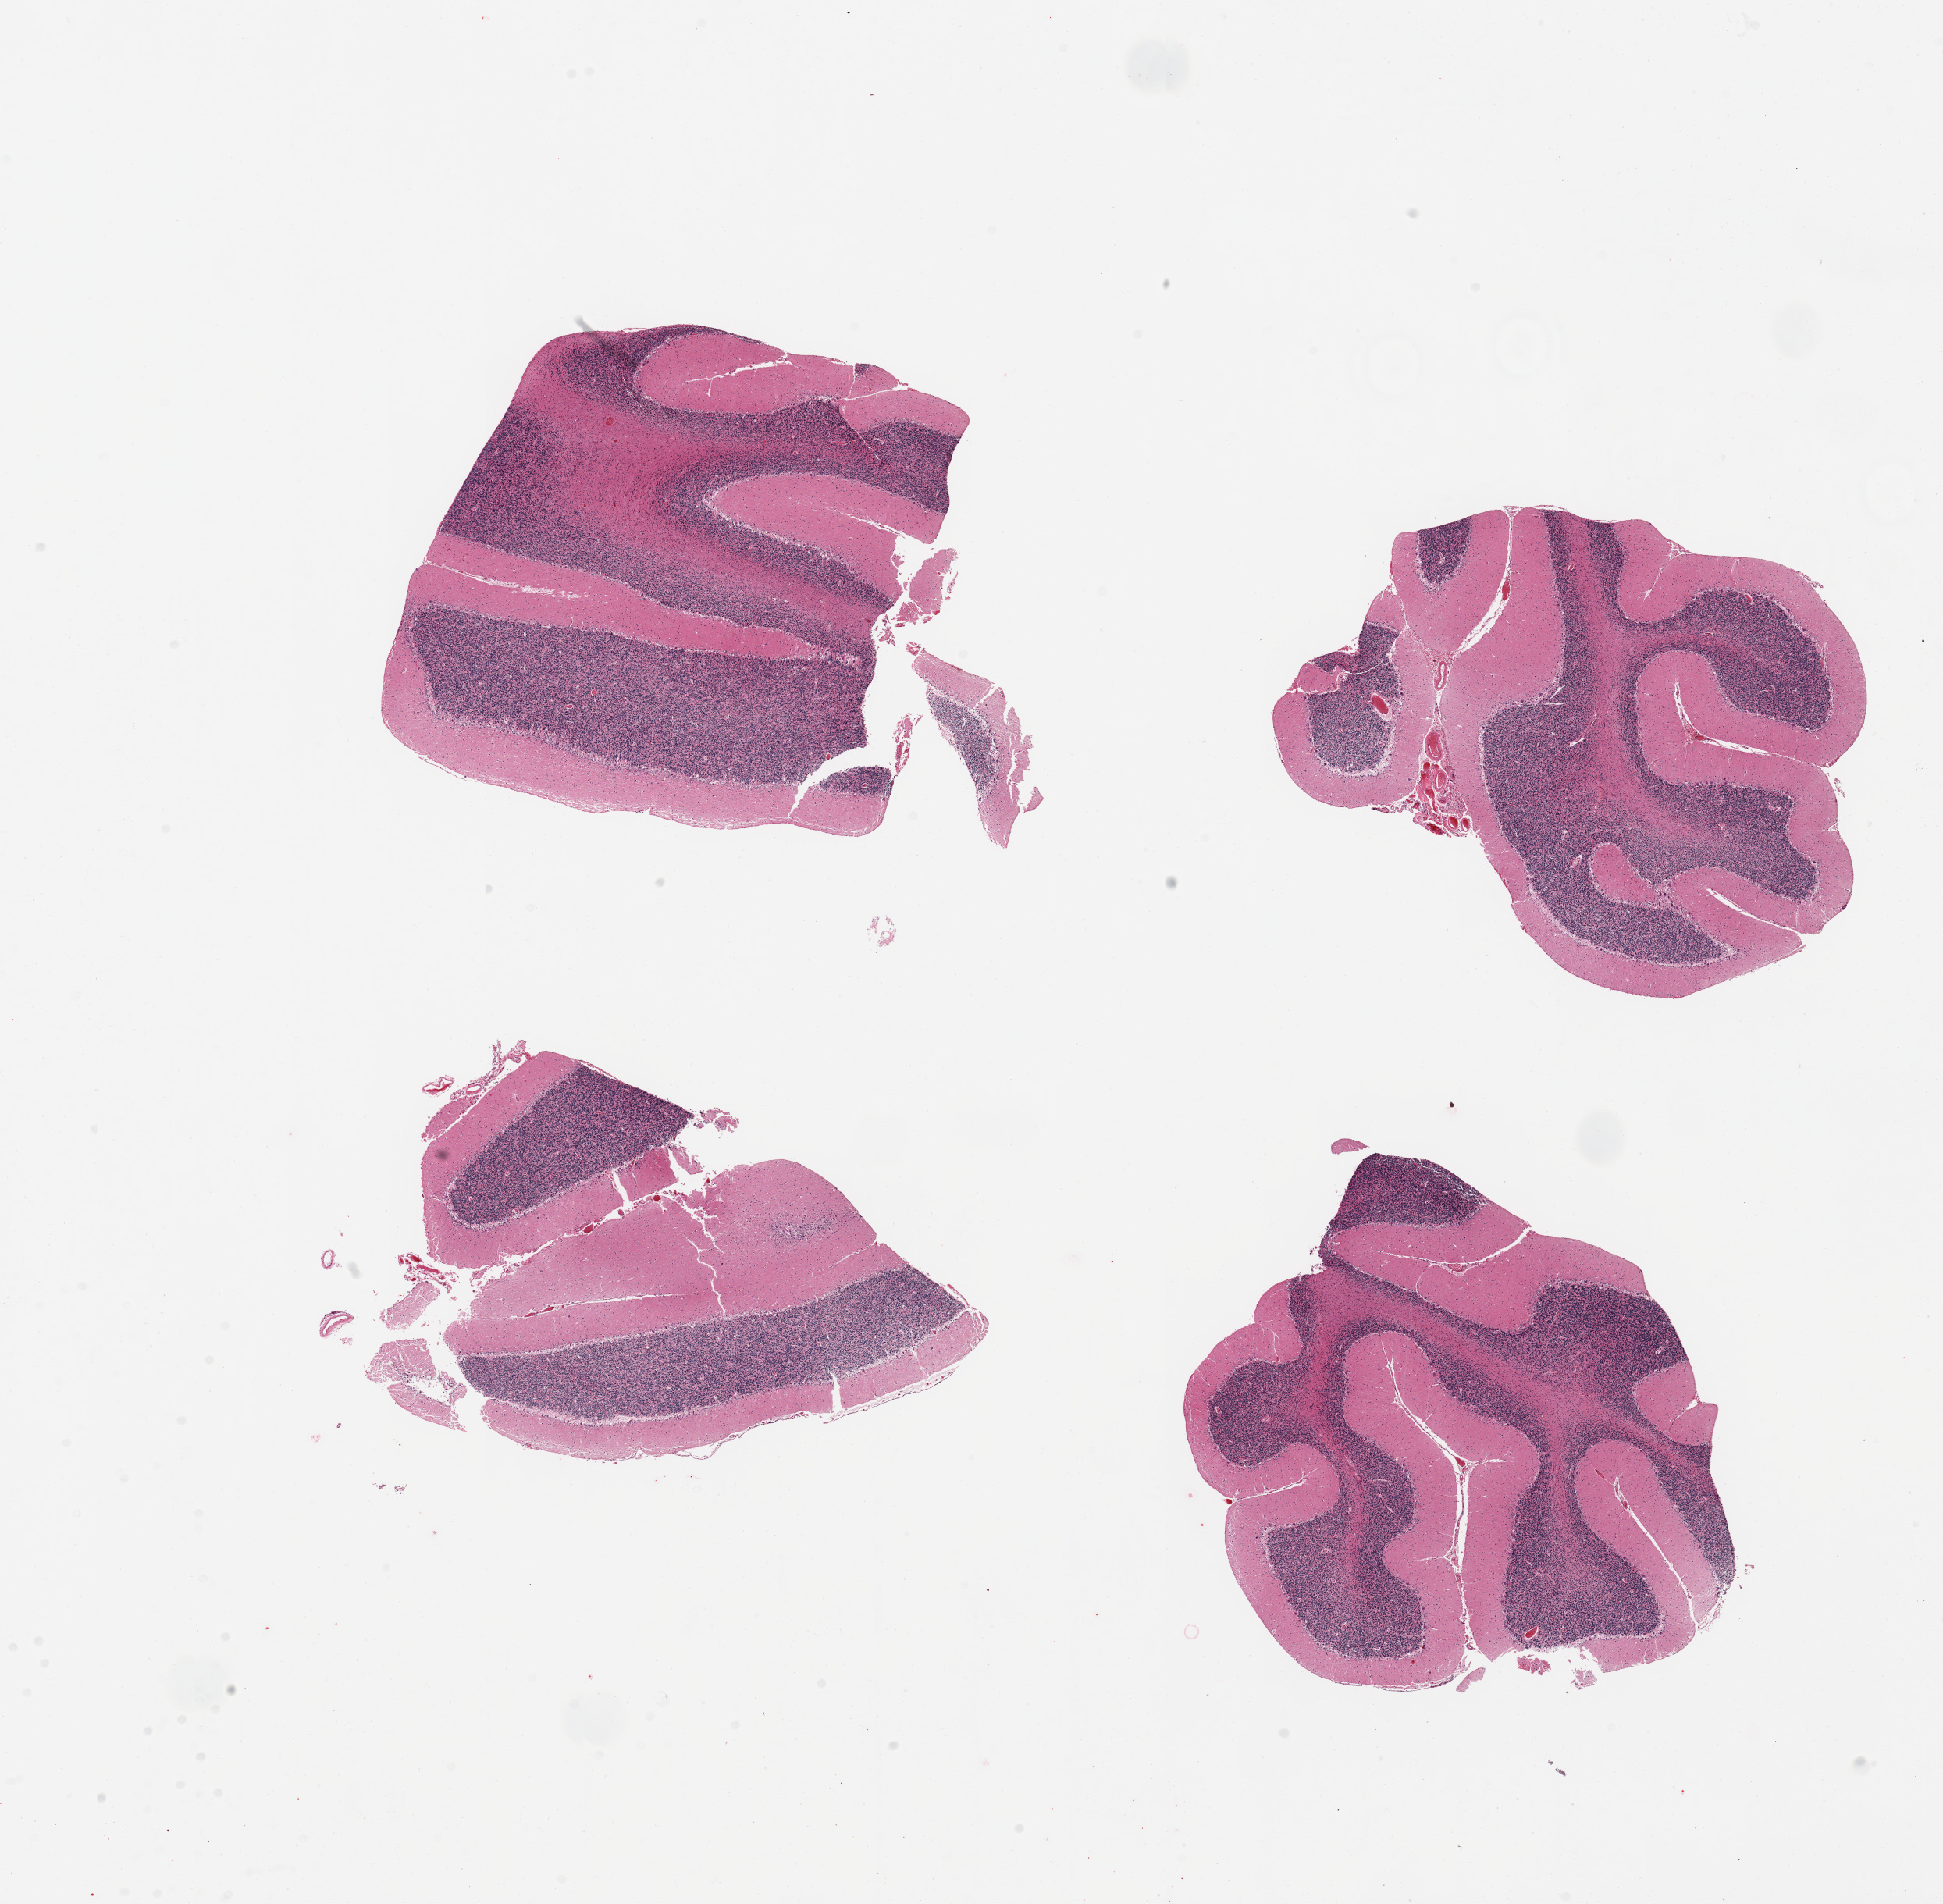
Digitized hematoxylin and eosin (H&E)-stained section, low-resolution overview of the scanned area, about 19.7 x 19.3 mm; PAXgene-fixed paraffin-embedded (PFPE) section; section of cerebellum (target tissue); donor tissue sample.
• review note (as recorded): 4 pieces